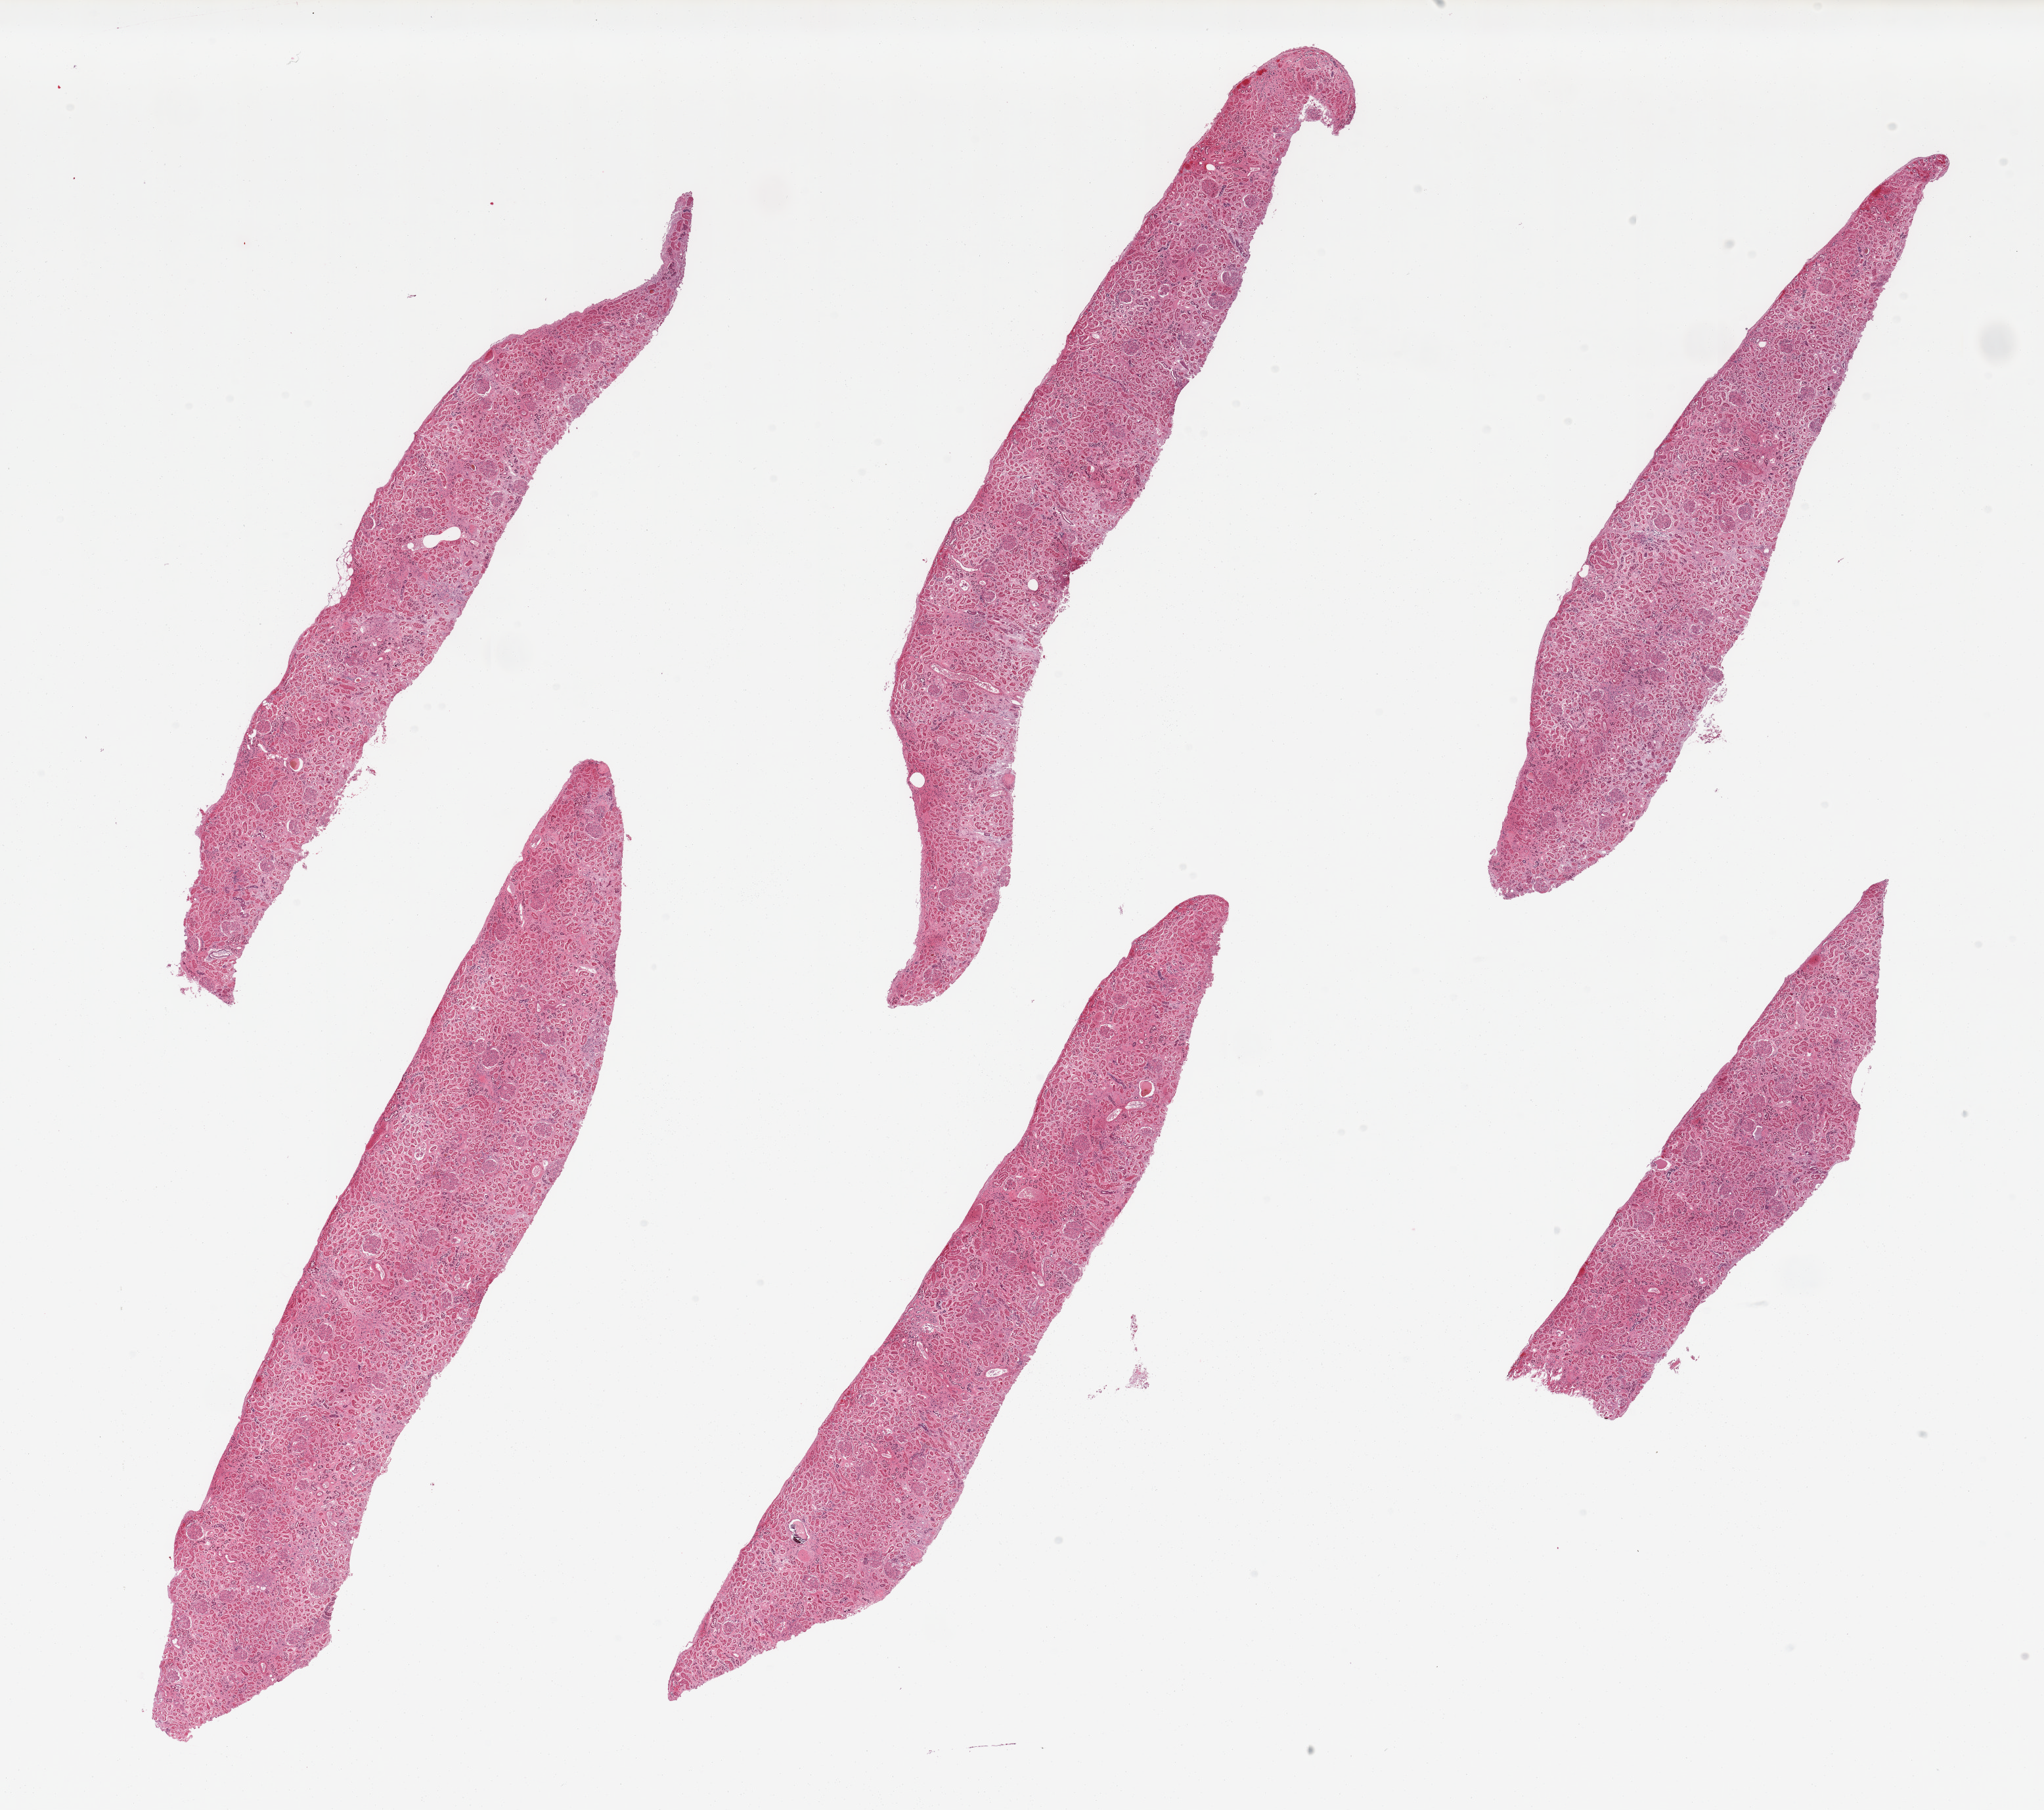
Digitized hematoxylin and eosin (H&E)-stained section — shown as a low-resolution overview of the whole scanned area (about 24.6 x 21.8 mm), PAXgene-fixed paraffin-embedded (PFPE) section, target tissue: renal cortex, tissue donor sample. Donor sex: male.
Reviewer comment on this tissue sample: 6 pieces; autolyzed distal tubules; arteriosclerosis and scattered hyalinized glomeruli; interstitial fibrosis; membranoproliferative glomerular changes.